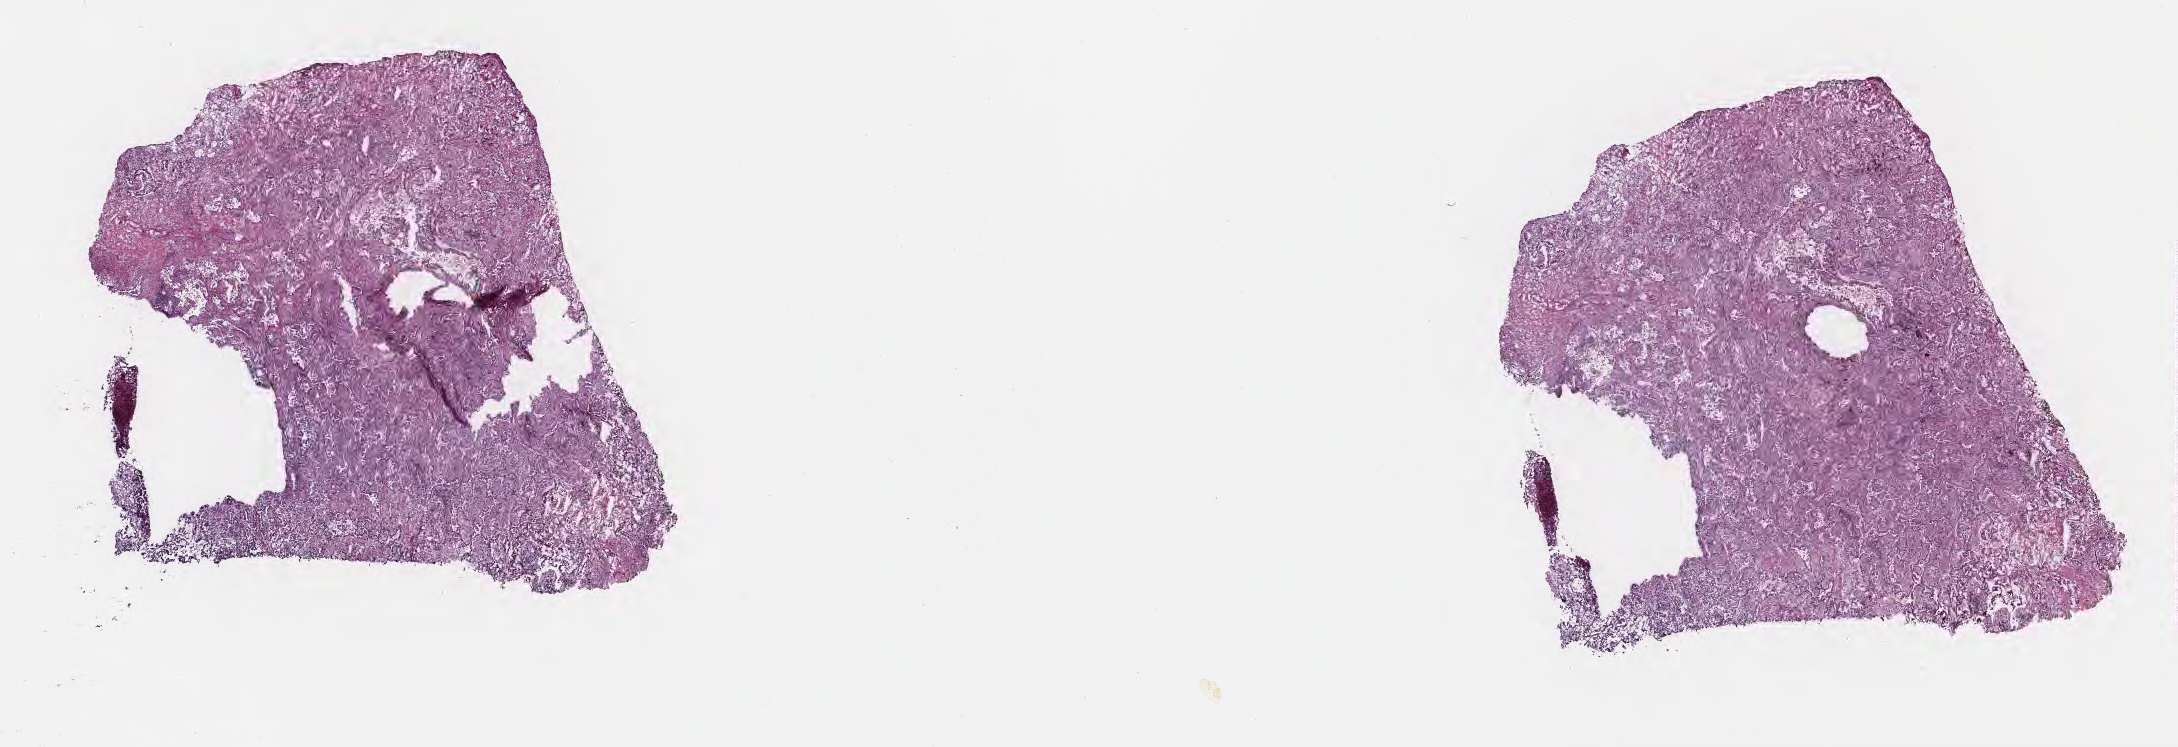
H&E whole-slide image — shown as a low-resolution overview of the whole scanned area (about 17.6 x 6.0 mm), frozen section, specimen: primary tumor, anatomic site: upper lobe of right lung. Patient male; aged 60. Composition of this section per pathologist review: tumor cells 50%, tumor nuclei 60%, stromal cells 50%, necrosis 0%, normal cells 0%. Inflammatory infiltration, as recorded: lymphocyte infiltration 50%, monocyte infiltration 50%, neutrophil infiltration 0%.
Section: top of the tissue portion. Histologic diagnosis: Adenocarcinoma with mixed subtypes. AJCC pathologic stage: Stage IIA.